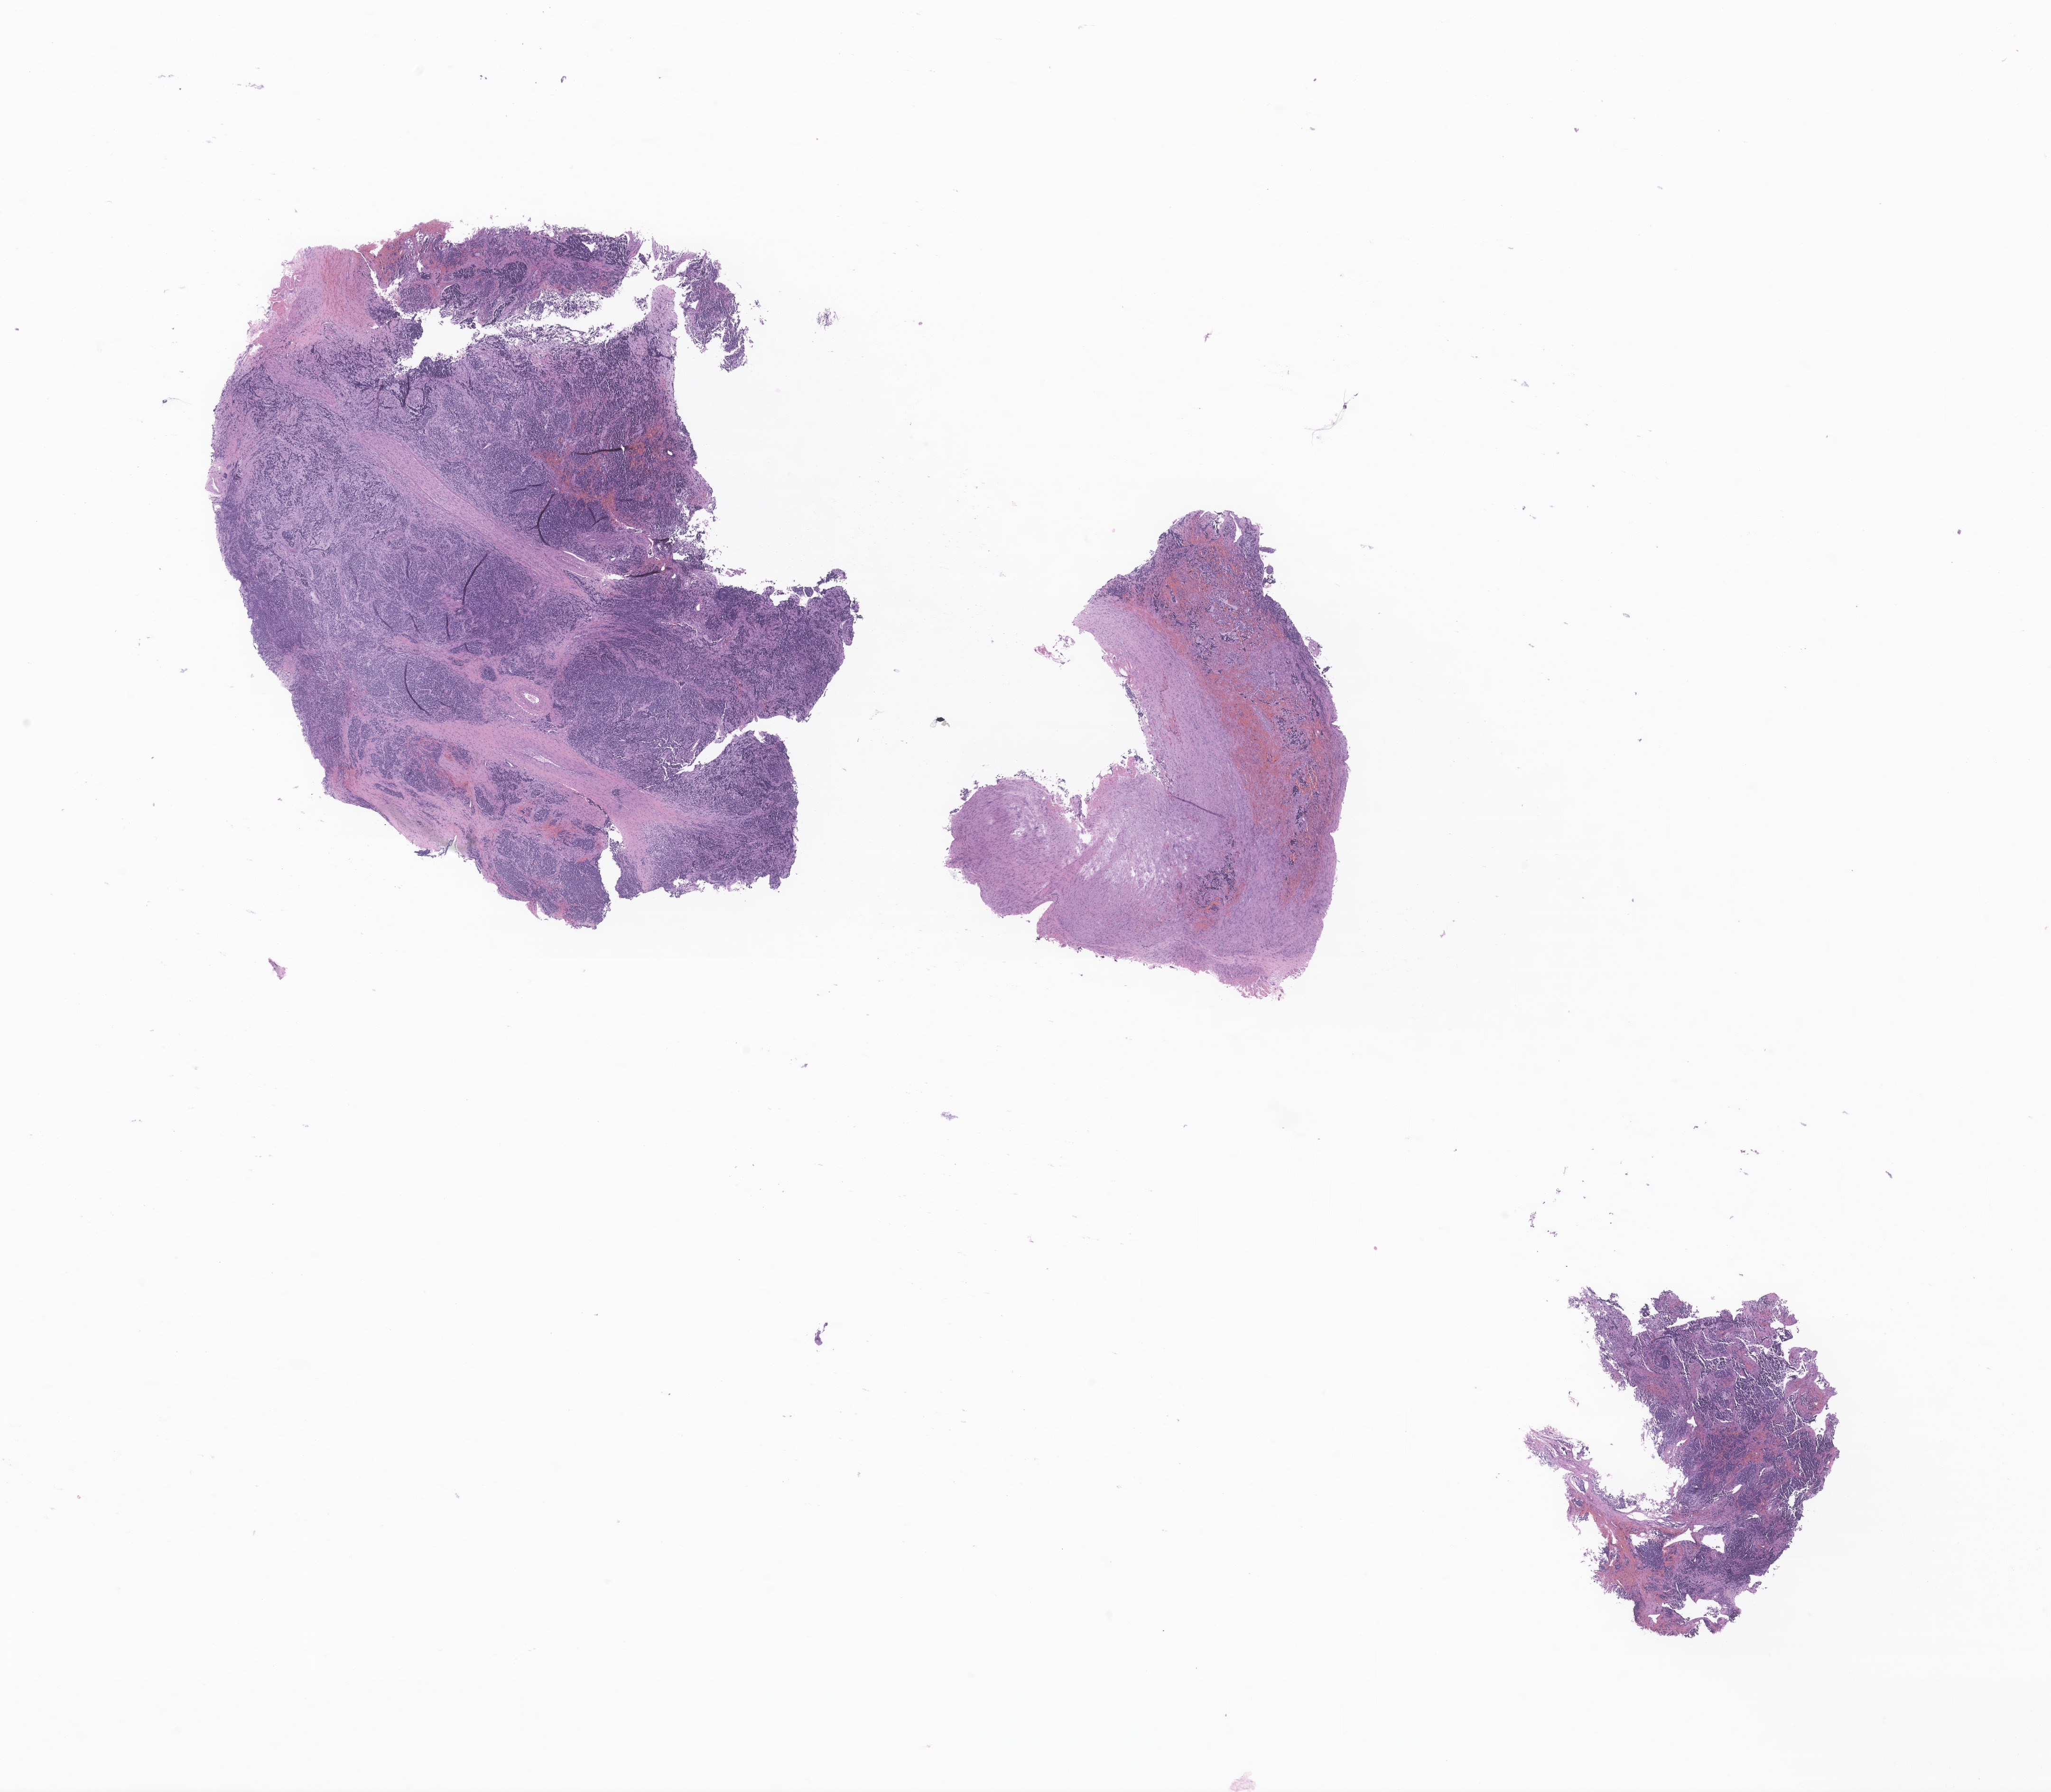
Haematoxylin and eosin whole-slide image of tumor tissue from the retroperitoneum, a low-resolution overview of the entire scanned area, about 18.2 x 15.9 mm, formalin-fixed paraffin-embedded section. Female patient, age 166 days.
* recorded diagnosis: Neuroblastoma, NOS